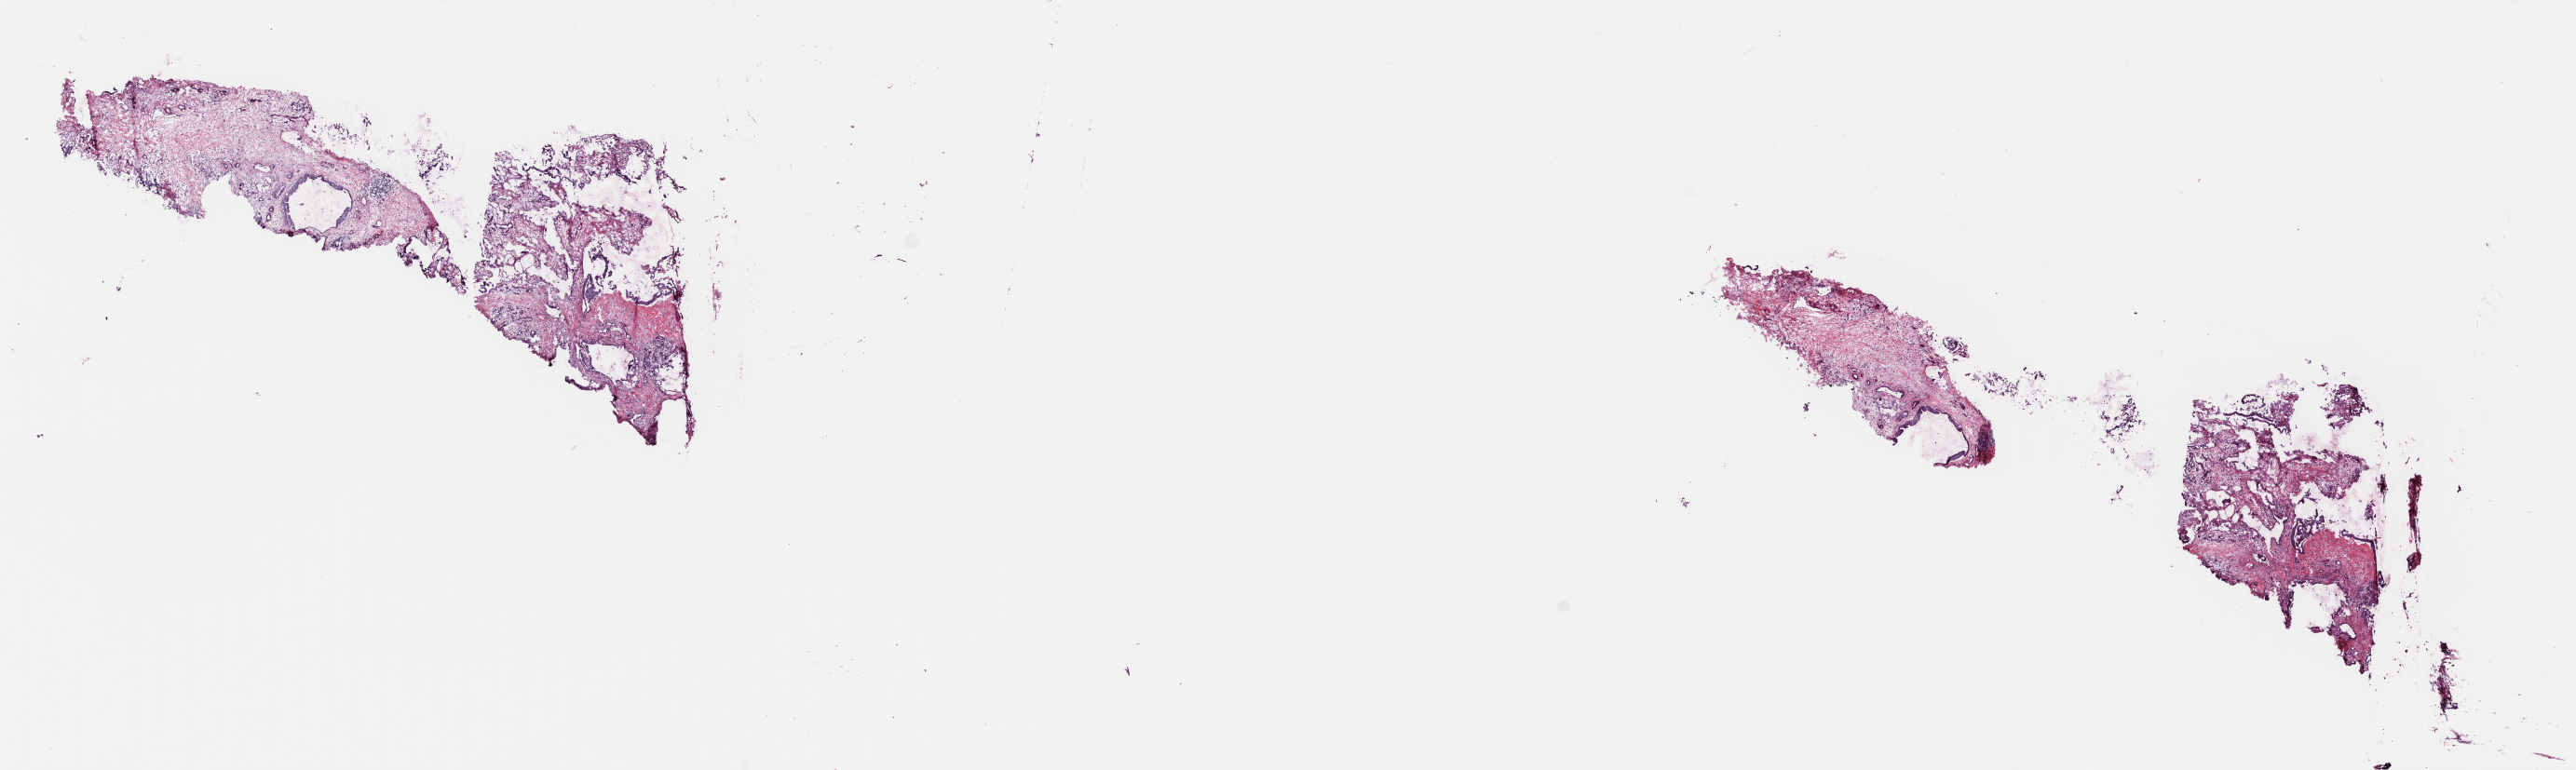
Whole-slide histology image, H&E-stained, whole scanned area (about 21.7 x 6.5 mm) shown as a low-resolution overview, frozen section, sample: primary tumour, pancreas. Patient: male, age at initial diagnosis 73 years. Histologic grade: G3 (poorly differentiated). Slide review estimates, as recorded: tumour cells 20%, tumour nuclei 50%, normal cells 0%, stromal cells 76%, necrosis 4%. Infiltration values recorded for this section: lymphocyte infiltration 8%, monocyte infiltration 1%, neutrophil infiltration 1%.
- TNM: T3 N1 MX
- diagnosis: Adenocarcinoma, NOS (head of pancreas)
- AJCC pathologic stage: IIB